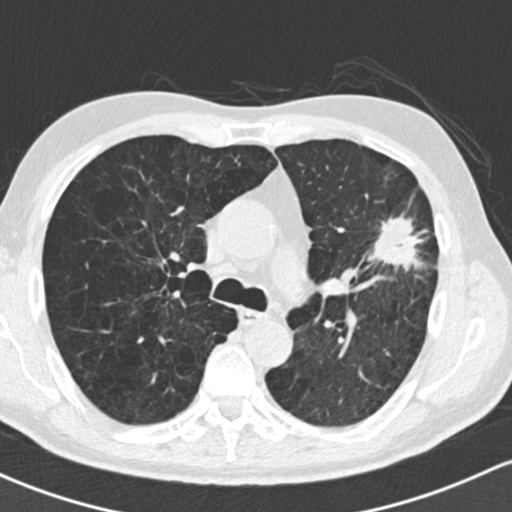
Low-dose screening chest CT, axial slice; baseline annual screen; lung window (W 1500 / L -600 HU); 120 kVp; slice 63 of 162 in the series. Male participant, aged 61 years at enrolment.
Expert reader's lesion annotation, bounding box (x1, y1, x2, y2) in pixels: (356, 186, 455, 294). The exam's reader record, not a measurement of the box and not confirmed to be the same lesion: non-calcified nodule or mass ≥4 mm, left upper lobe, 35 × 35 mm, spiculated (stellate) margins, soft tissue attenuation. Later outcome: lung cancer diagnosed 19 days after this screen — adenocarcinoma, NOS, left upper lobe, well differentiated (G1), stage IIIA (AJCC 6th edition), 45 mm at pathology.